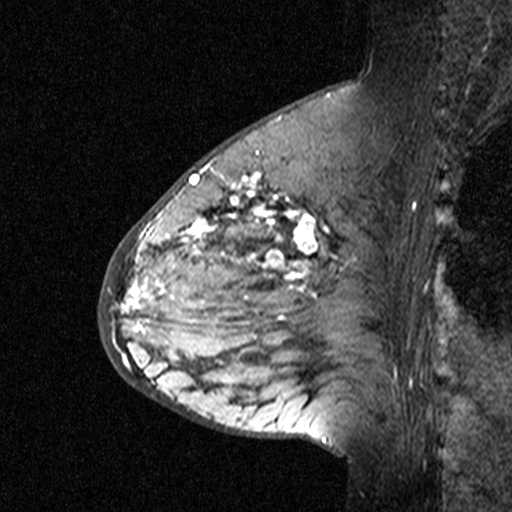
Breast MRI (dynamic contrast-enhanced), one sagittal slice; position 17 of 44 along the scan axis; dynamic contrast-enhanced study with each time point stored as its own series, time point 3 of 4 at this slice position (ordered by acquisition time); 1.5 T; TE 4.5 ms, TR 11 ms; 3 mm slice thickness; 512 × 512 image matrix. Patient: female, 65 years. Case-level facts recorded for this patient, not image findings: setting: breast cancer imaged before/during neoadjuvant chemotherapy; receptor status: HER2-positive.
Structures marked on this image (semi-automatically segmented with operator editing):
- analysis volume of interest (the breast-tissue region the enhancement analysis was run in; not a lesion): bounding box [x1, y1, x2, y2] px = [182, 190, 353, 361]
- tumour enhancement mask (voxels above the 90 % enhancement threshold inside the analysis volume of interest): [182, 190, 316, 297]